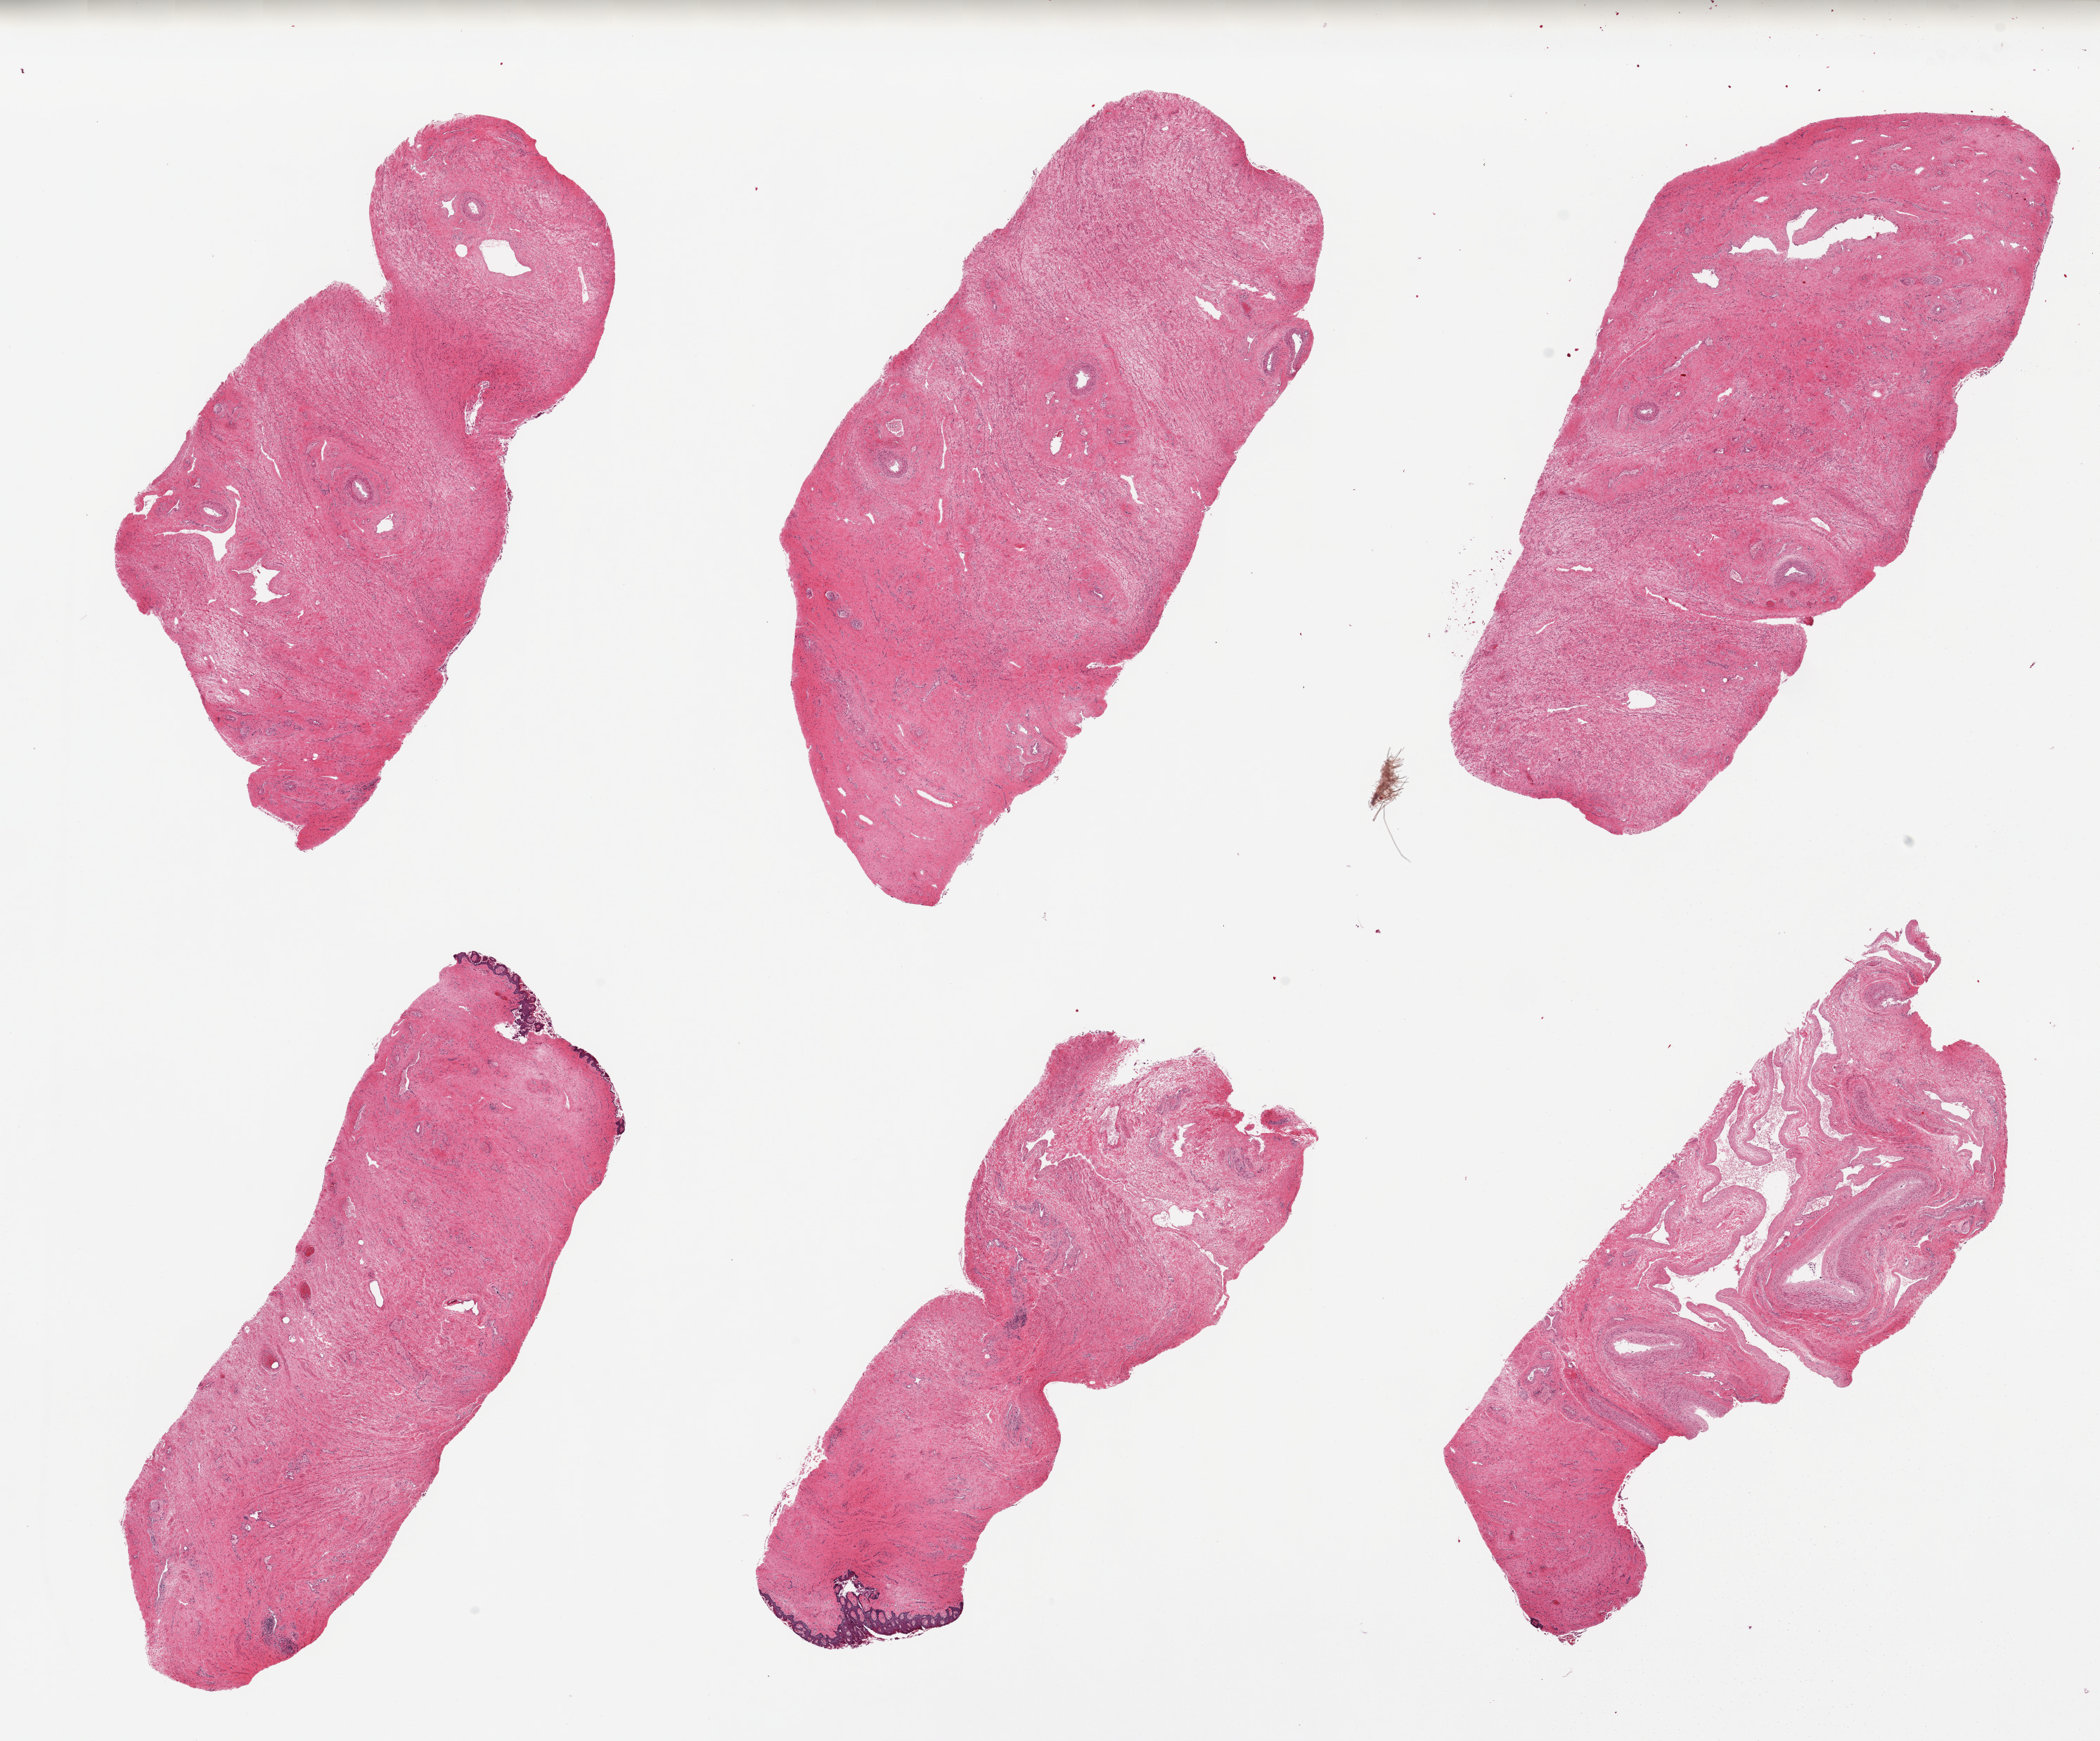
Digitized H&E-stained section, brightfield, low-resolution overview of the scanned area, about 23.6 x 19.6 mm (acquisition: 20x scan), PAXgene-fixed, paraffin-embedded tissue, target tissue: vagina, tissue donor sample.
• review note (as recorded): 6 pieces, 99% stroma, trace sloughing autolyzed squamous mucosa